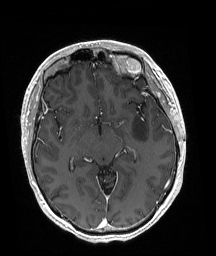
Brain MRI from a brain-tumour surgery series, one axial slice; position 110 of 192 along the scan axis; T1-weighted post-contrast; 216 × 256 image matrix, field of view 211 × 250 mm. From the clinical record (not read from this slice): histopathology: Astrocytoma; WHO grade: 3; IDH mutation: yes.
Structures marked on this image (outlined manually by an expert reader):
- tumour: bounding box (x1, y1, x2, y2) in pixels: (132, 115, 148, 141)